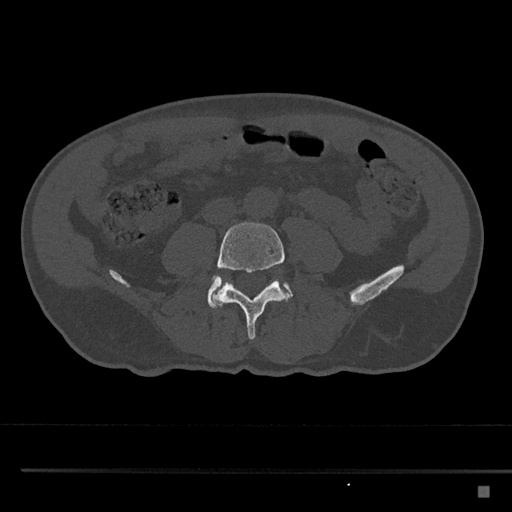
CT including the spine, one axial slice; position 628 of 797 along the scan axis; reconstruction kernel Br40s/3; bone window (W 1800 / L 400 HU); 0.5 mm slice thickness; 512 × 512 image matrix, field of view 391 × 391 mm. Patient: male, 59 years. From the clinical record (not read from this slice): primary cancer: prostate.
Annotated regions visible in this slice (semi-automatic segmentation, software-assisted and operator-edited):
- L4 vertebra: box from (x=212, y=222) to (x=290, y=340) px
- L5 vertebra: (x=207, y=275)–(x=294, y=309)